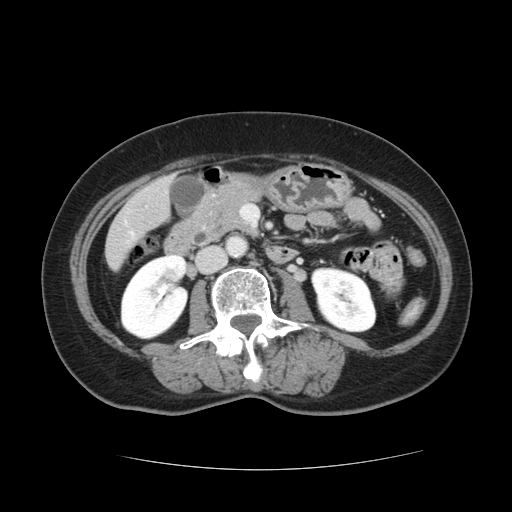
Contrast-enhanced abdominal CT, one axial slice. Position 31 of 128 along the scan axis. 120 kVp. Intravenous contrast given. Soft-tissue window (W 400 / L 40 HU). 512 × 512 image matrix, field of view 366 × 366 mm. Female patient, age 67 years. Case-level facts recorded for this patient, not image findings: diagnosis: colorectal cancer liver metastases, imaged before liver resection; multiple liver metastases: yes.
Annotated regions visible in this slice (manually delineated by an expert):
- liver: bounding box [x1, y1, x2, y2] px = [106, 179, 171, 268]
- planned liver remnant (the part of the liver to remain after resection): [106, 213, 138, 268]